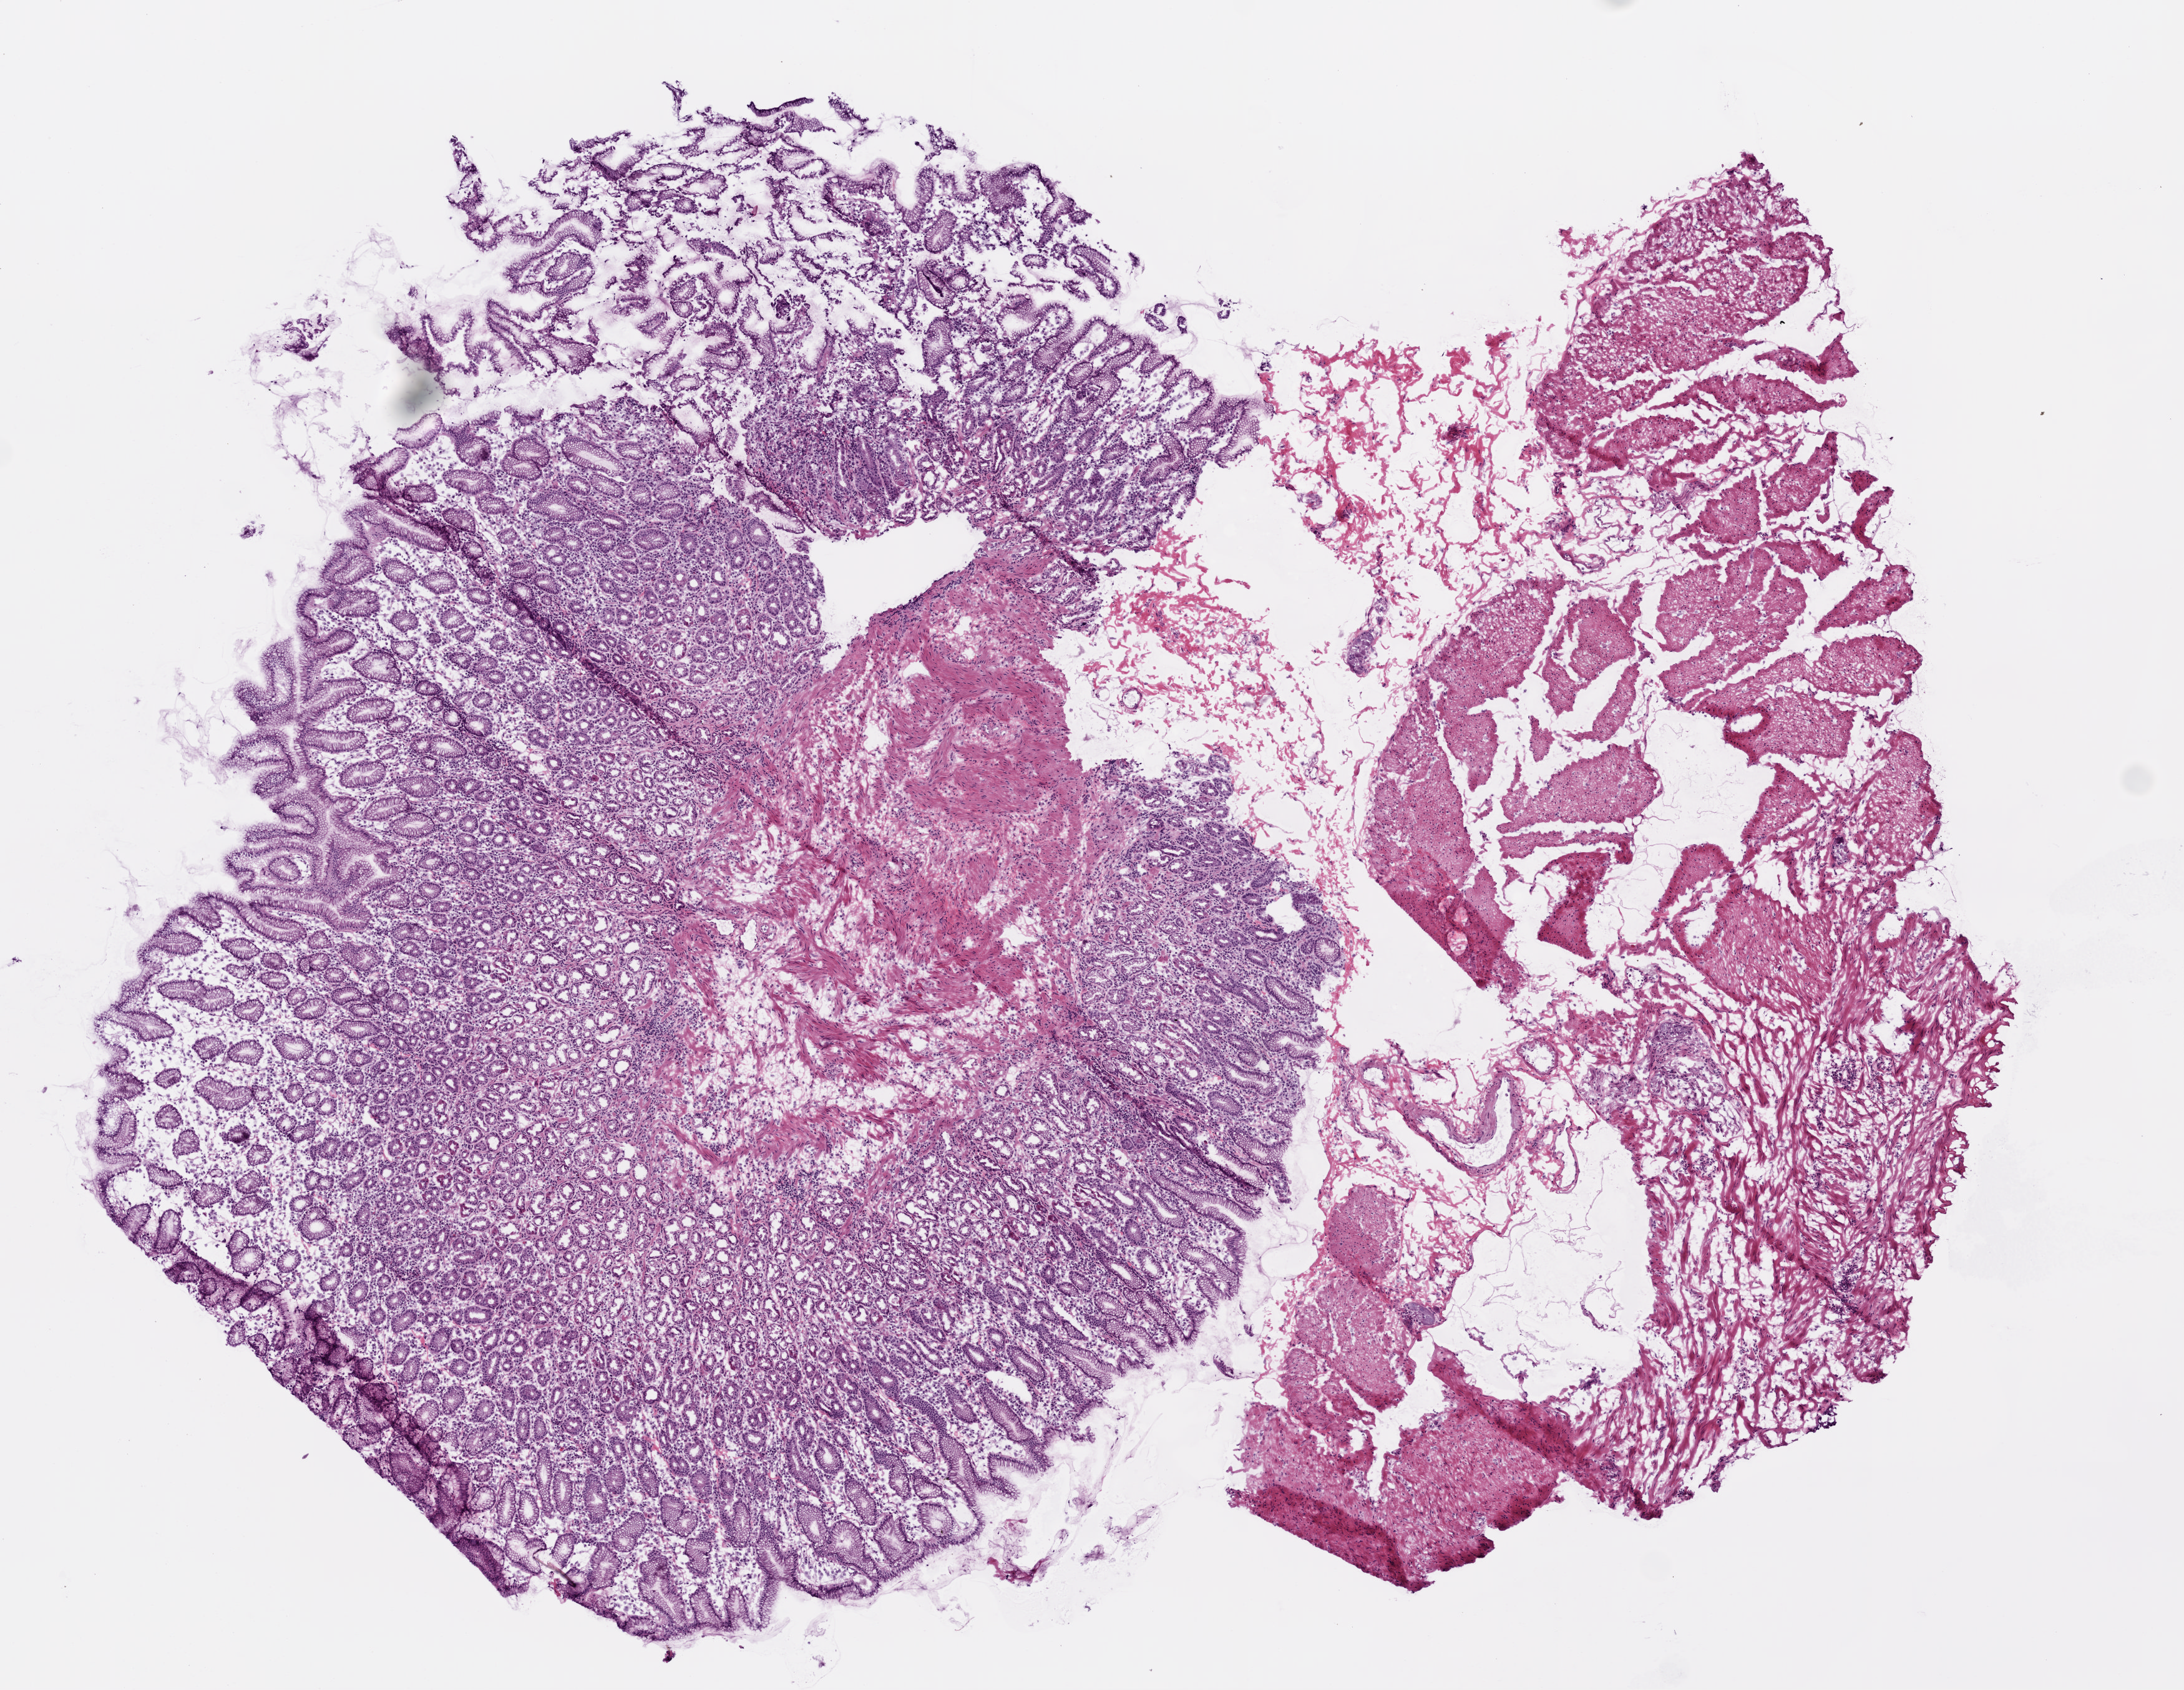
Whole-slide histology image, H&E, low-resolution overview of the scanned area, about 7.0 x 5.4 mm (acquisition: 20x scan), frozen section, solid tissue normal (non-tumour tissue) sample from the stomach. Patient: female, age at initial diagnosis 67 years.
This section: solid tissue normal sample (biorepository sample class). Patient diagnosis: Adenocarcinoma, intestinal type (body of stomach).